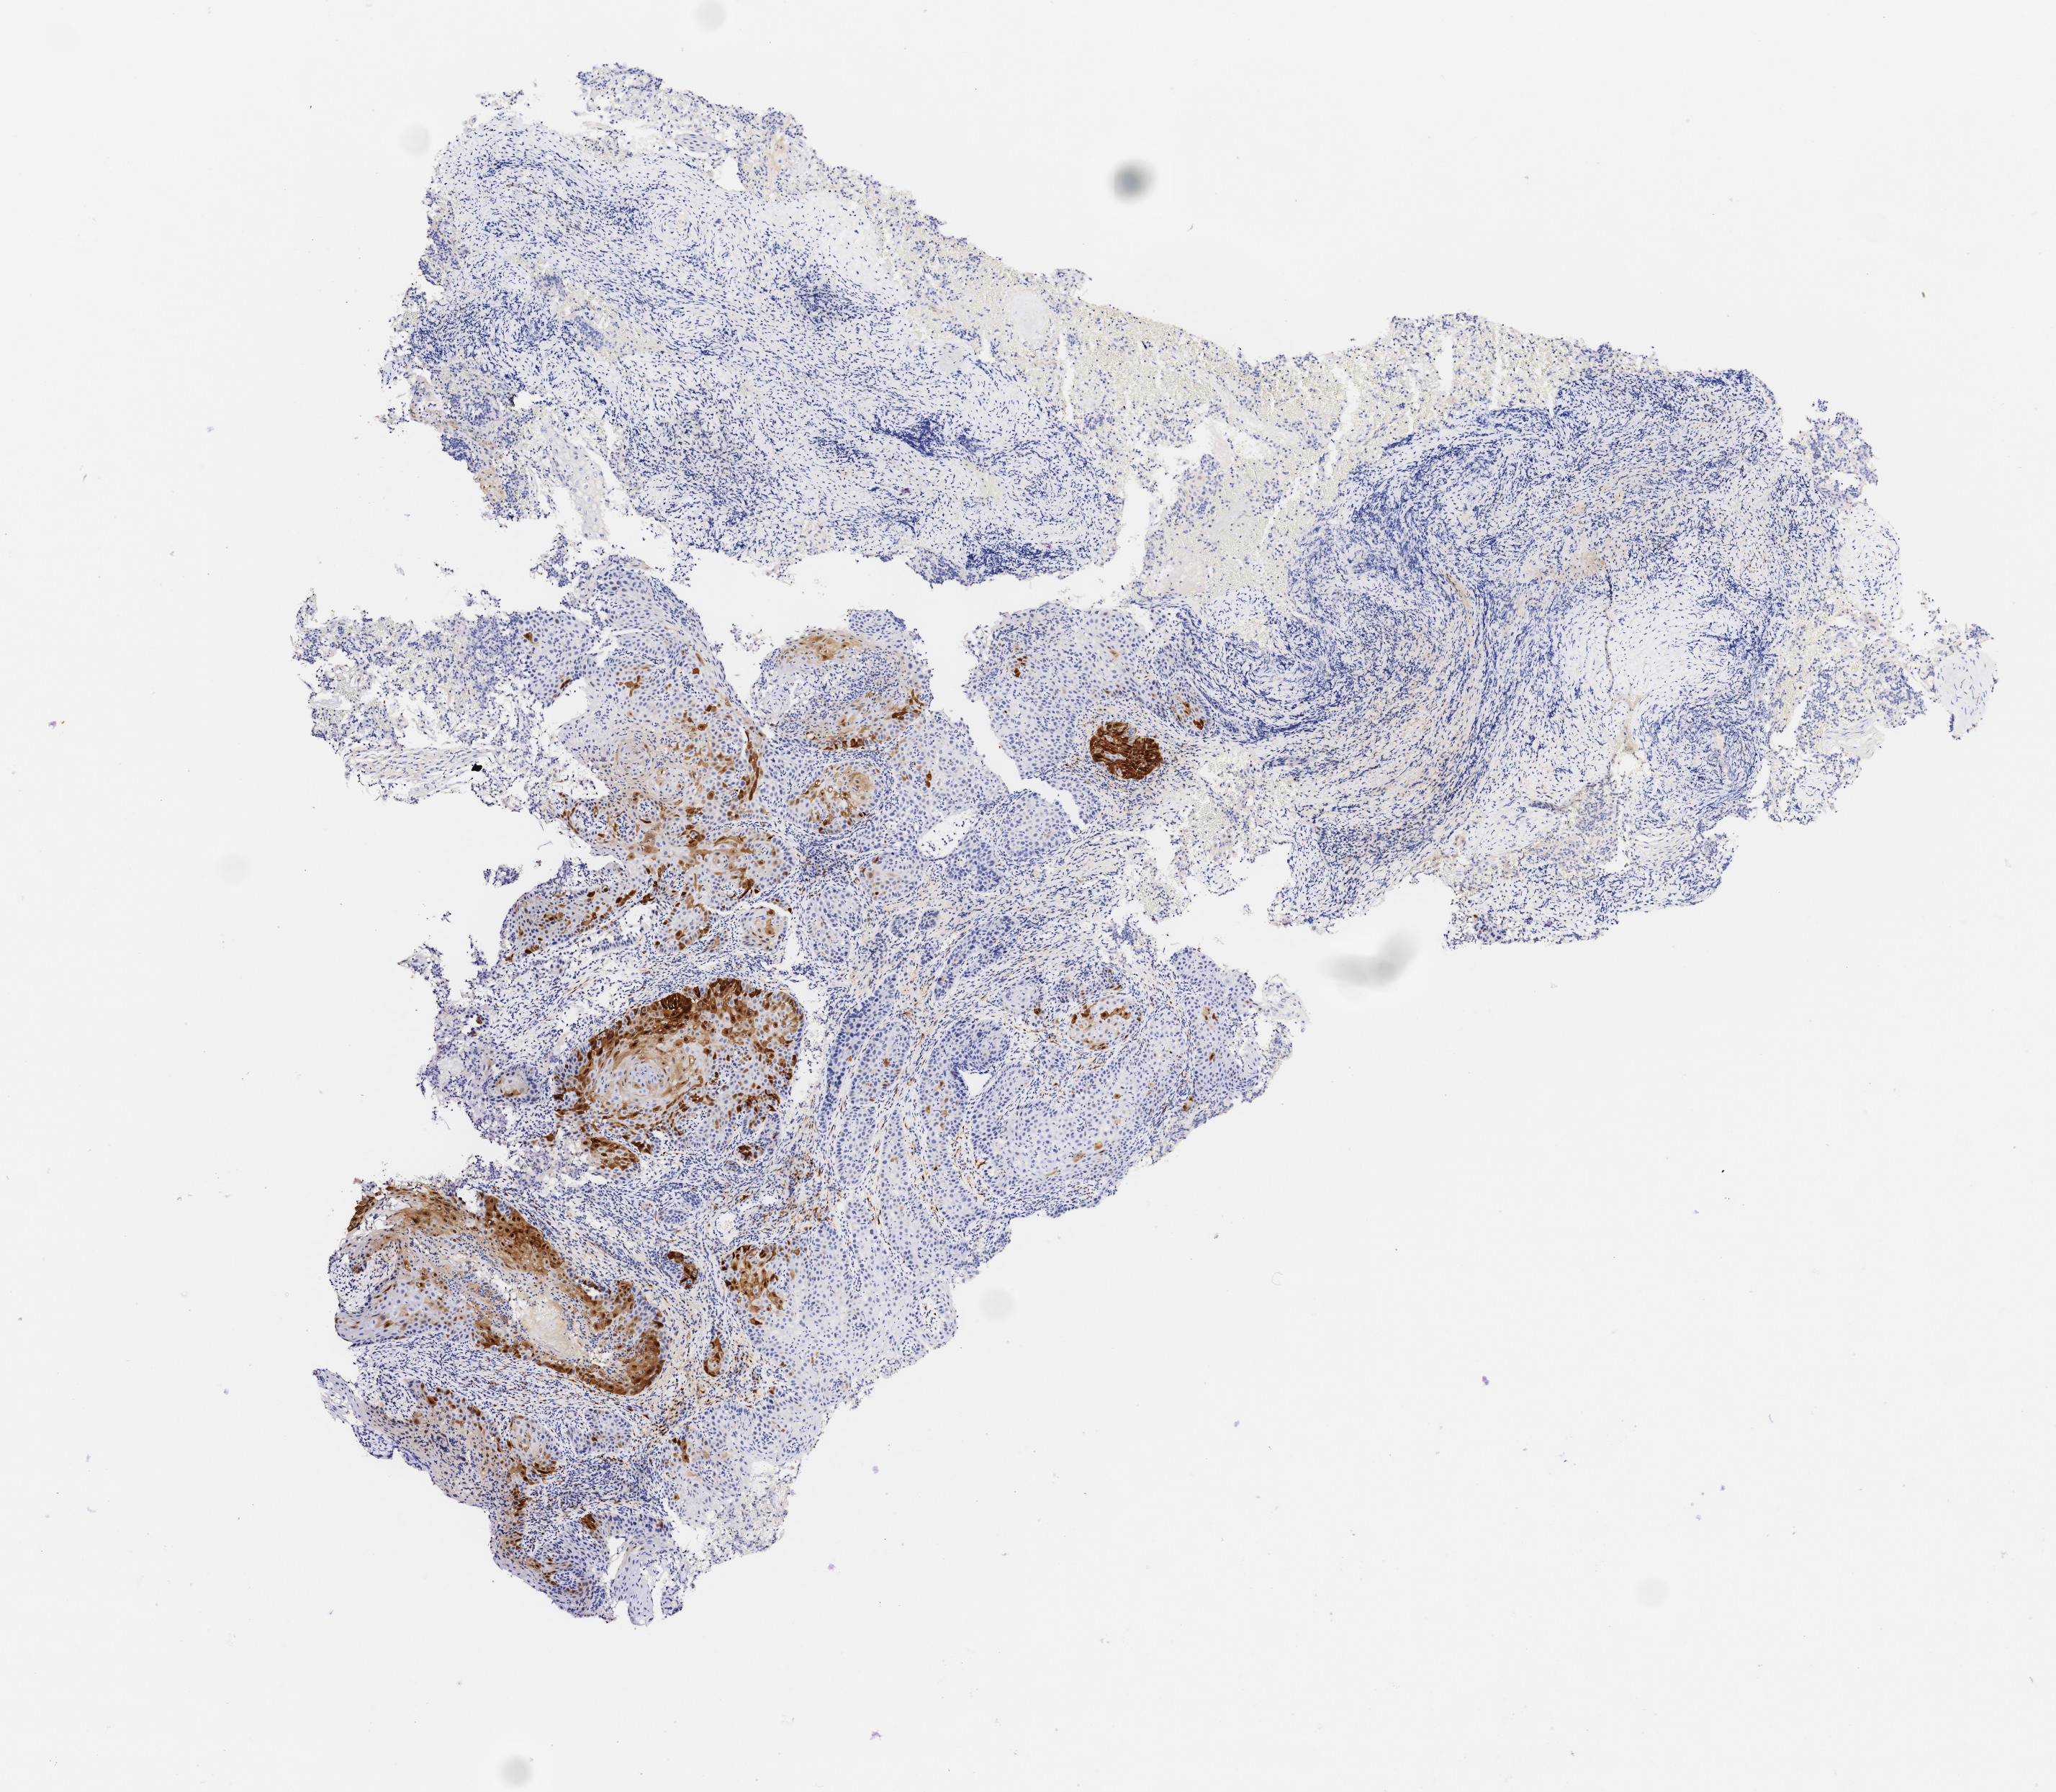
Whole-slide image, immunohistochemical stain for p16 (p16INK4a), a low-resolution overview of the entire scanned area, about 5.7 x 5.0 mm; specimen: tumor tissue; site: cervix. Female patient, 78 years old.
• histologic diagnosis: Squamous cell carcinoma, large cell, nonkeratinizing, NOS